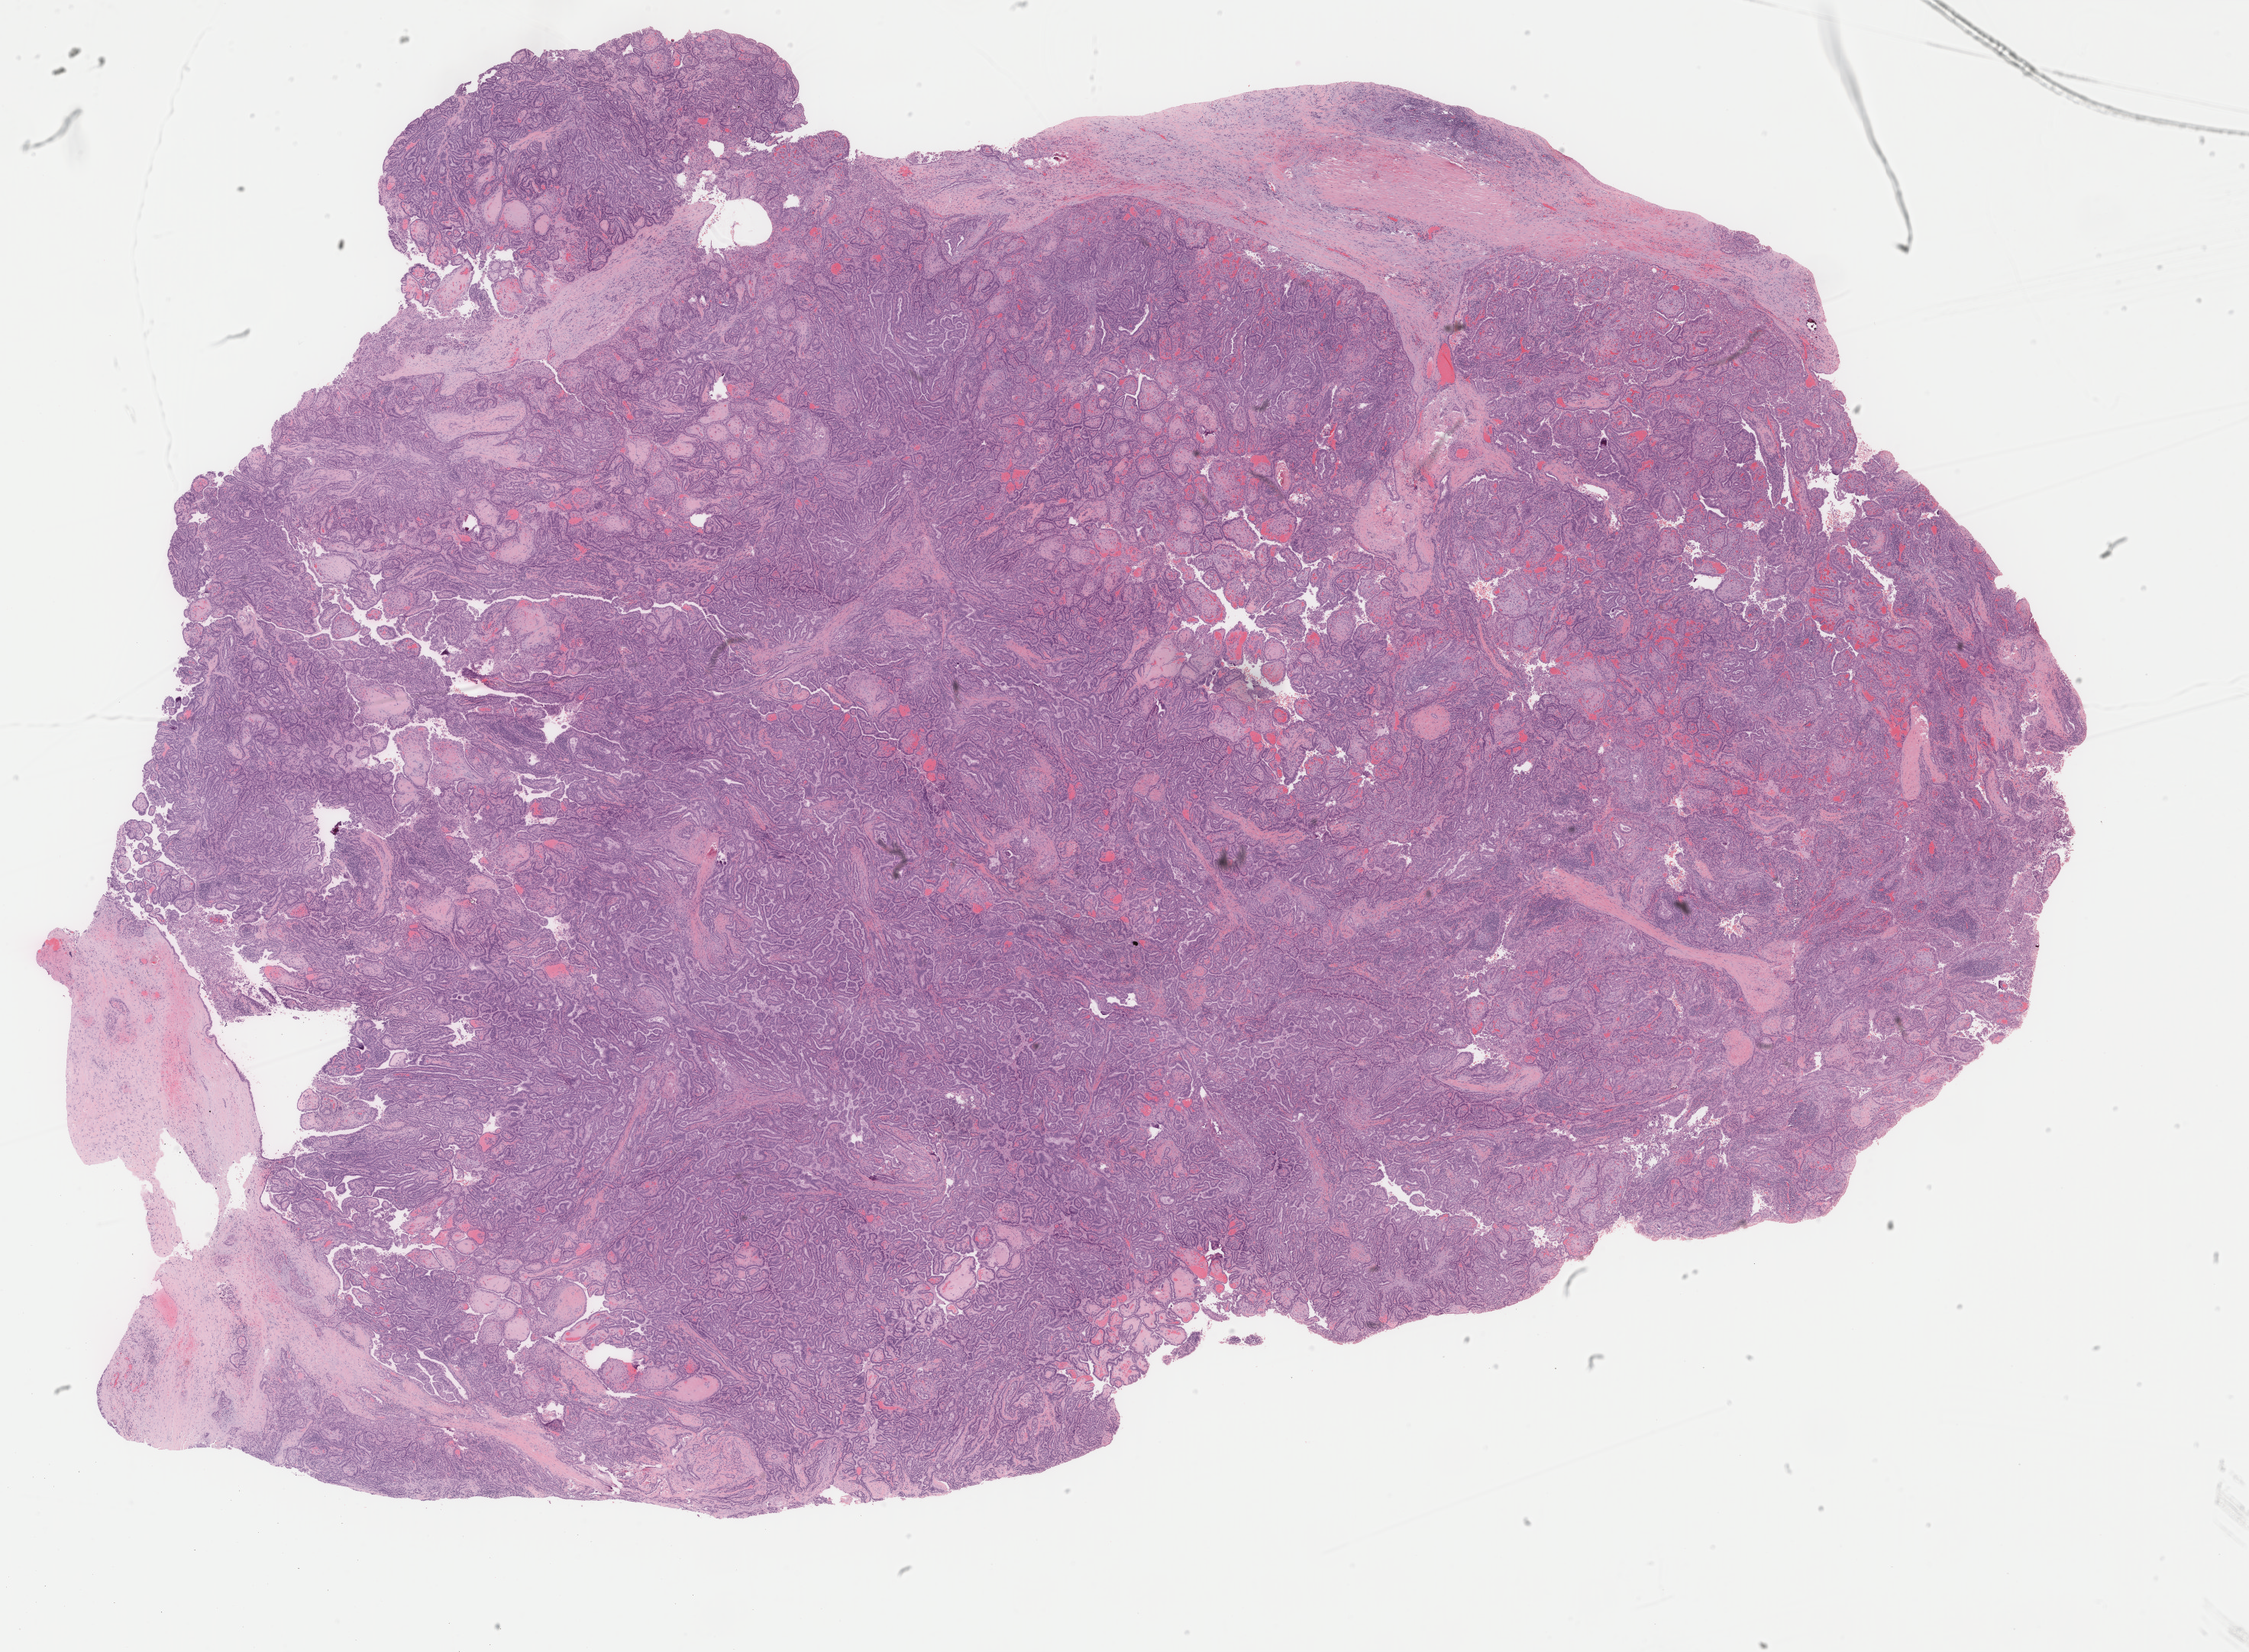
Digitized Hematoxylin and eosin (H&E) stained tissue section (whole slide) — shown as a low-resolution overview of the whole scanned area (about 23.4 x 17.2 mm, slide scanned at 40x). Formalin-fixed paraffin-embedded (FFPE) diagnostic section. Thyroid, primary tumour sample. Female, age 36 years at initial diagnosis.
• histologic diagnosis: Papillary adenocarcinoma, NOS
• lymph nodes positive (case pathology): 8 of 9 examined
• AJCC pathologic stage: I